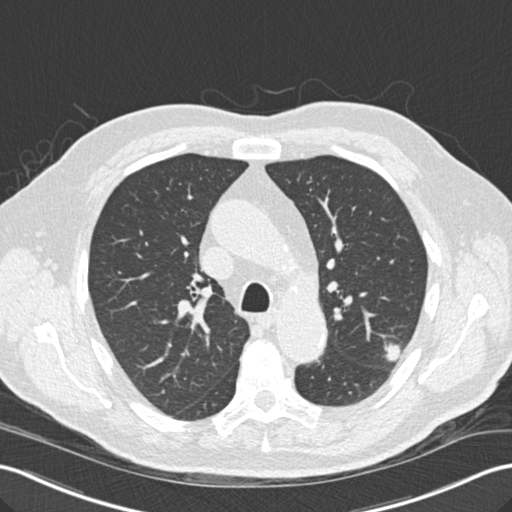
Low-dose screening chest CT, axial slice, third annual screen, lung window (W 1500 / L -600 HU). Male participant, aged 67 years at enrolment.
Expert-annotated lung lesion, bounding box [x1, y1, x2, y2] px = [365, 330, 414, 375]. The screening reader recorded 2 non-calcified nodules or masses ≥4 mm on this exam (left upper lobe, left lower lobe); which of them this box marks is not recorded. Official screen result: positive, other. Lung cancer was diagnosed 55 days after this screen: squamous cell carcinoma, large cell, nonkeratinizing, NOS, left upper lobe, moderately differentiated (G2), stage IA (AJCC 6th edition), 15 mm at pathology.